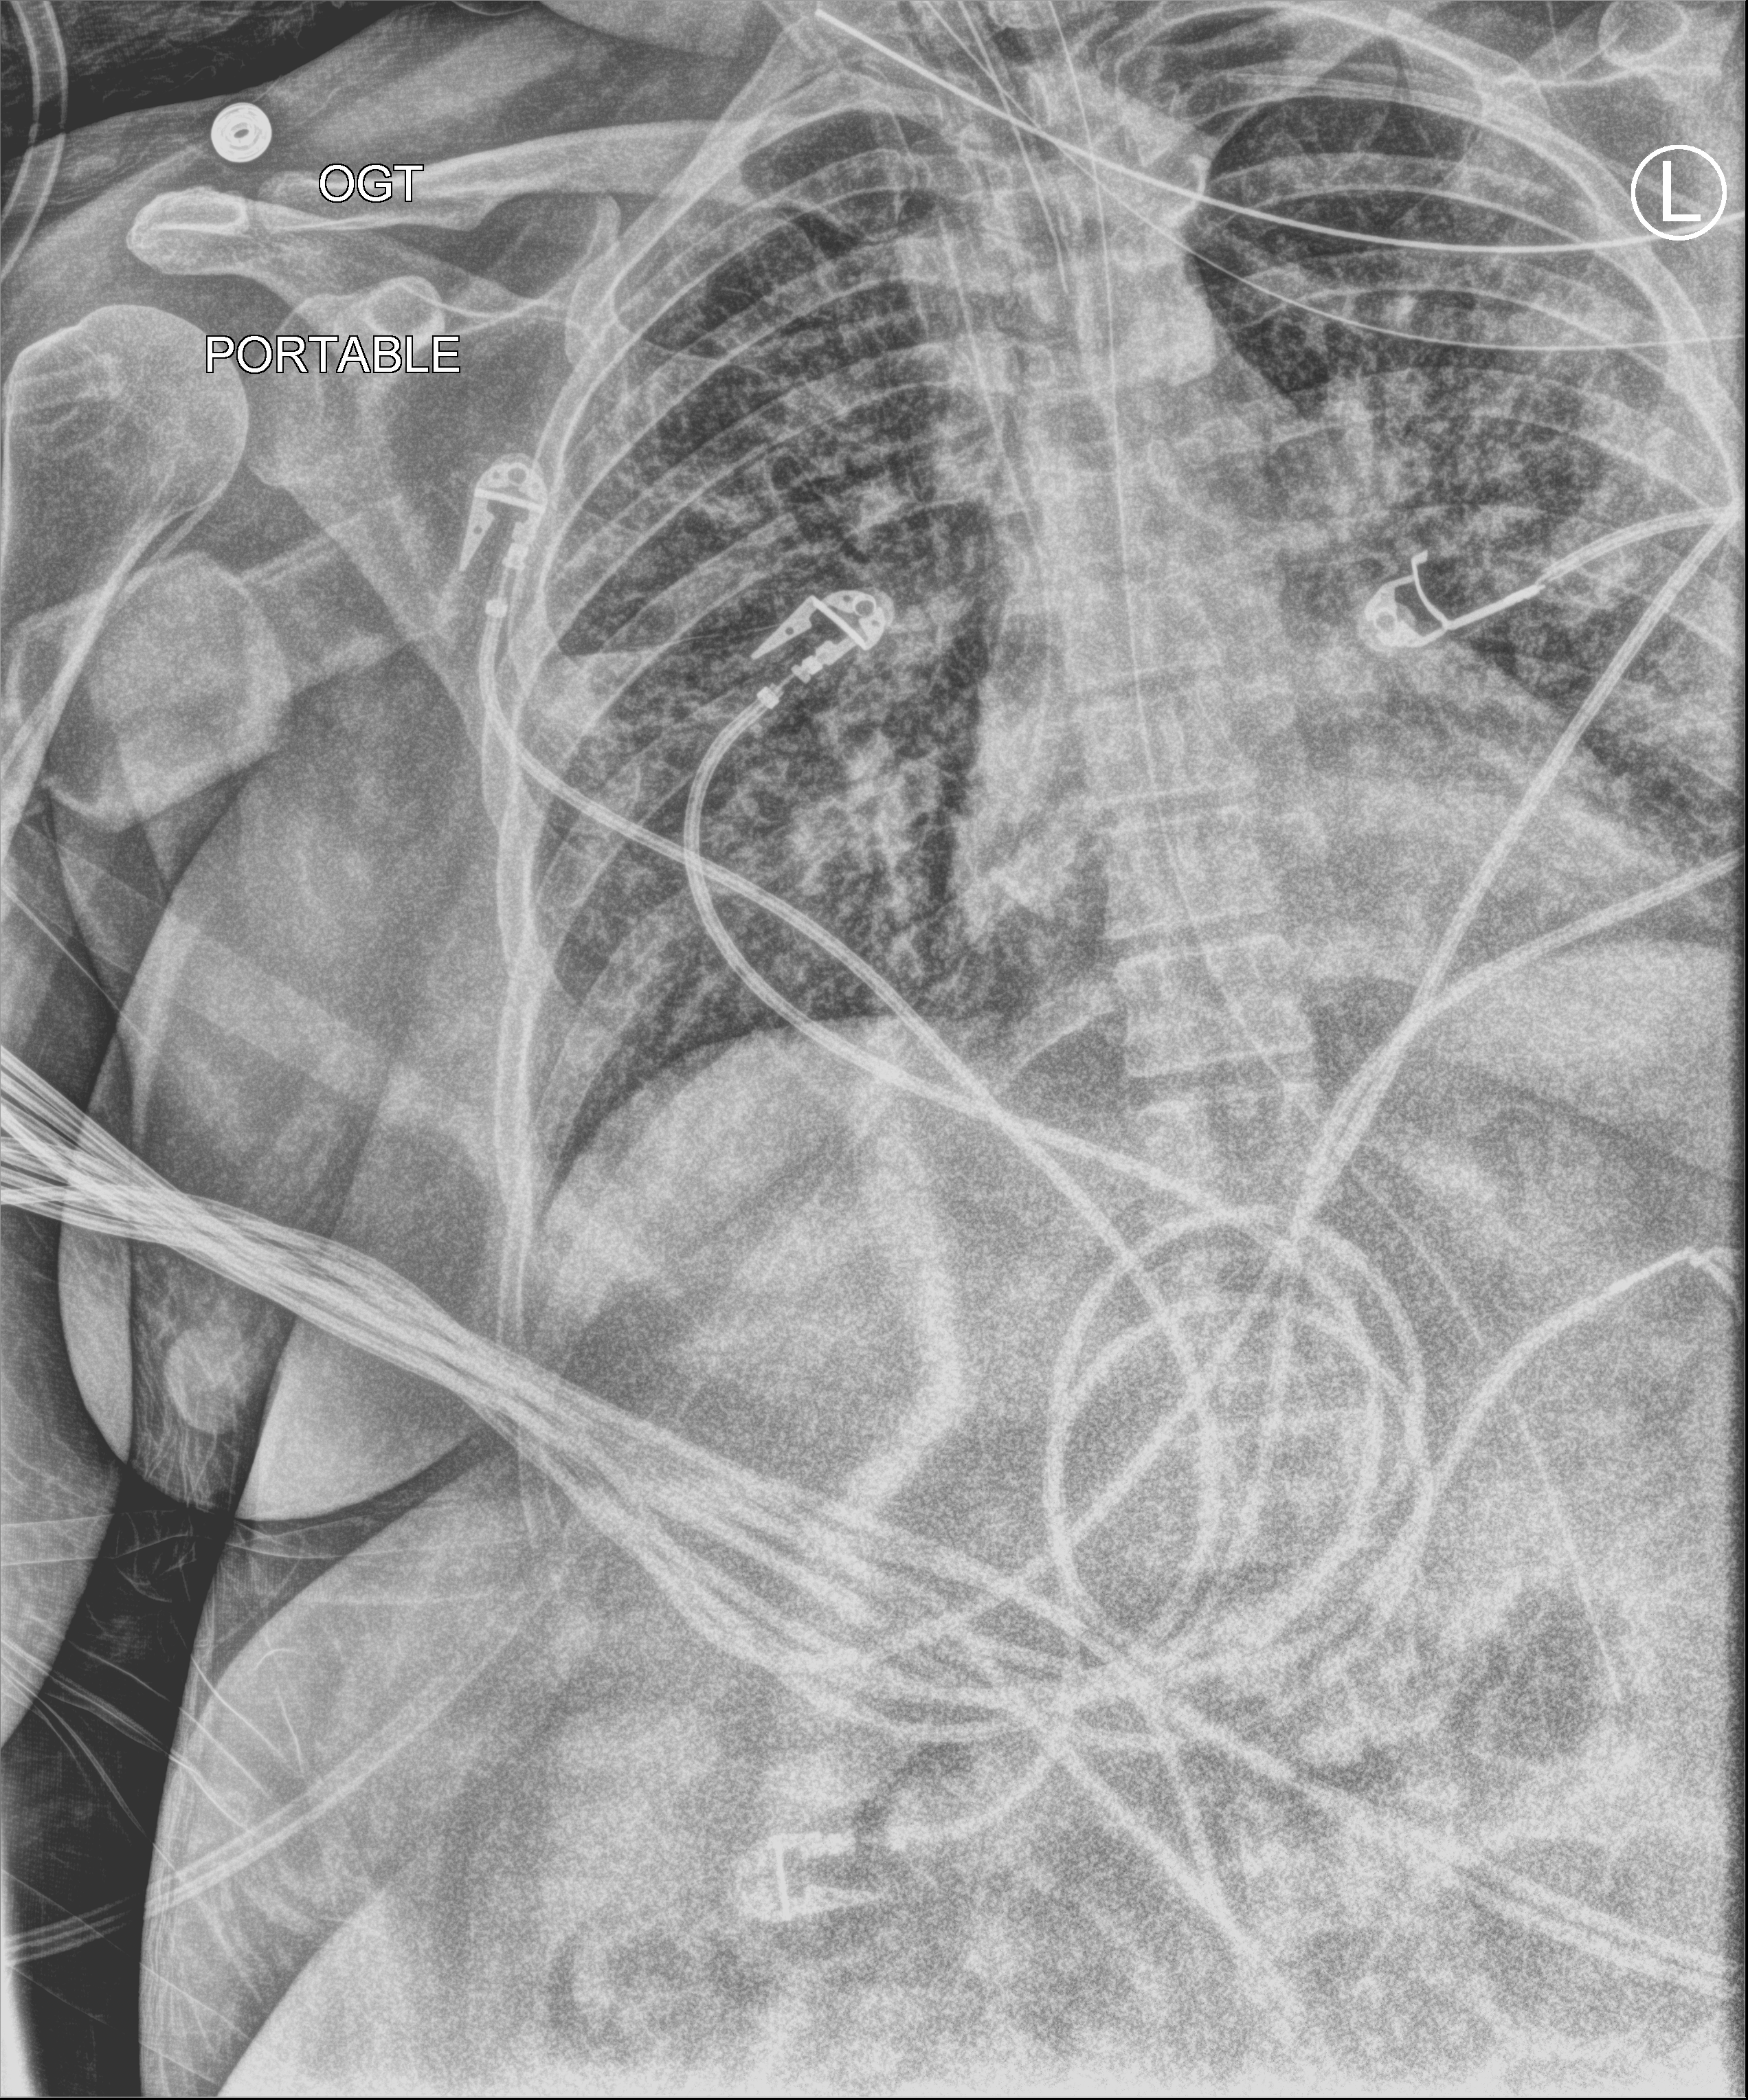
Bedside chest radiograph (computed radiography), anteroposterior (AP) projection. Female patient hospitalised with COVID-19, age 18–59 years.
Admission-level facts for this patient (not findings on this image; timing relative to this image not recorded): diabetes (admission record): yes; mechanically ventilated during this hospital stay: yes.